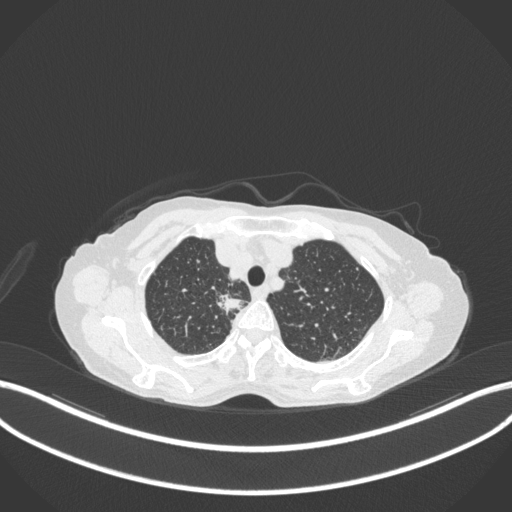
Chest CT, one axial slice. Position 309 of 363 along the scan axis. Reconstruction kernel B31f. 120 kVp. Lung window (W 1500 / L -600 HU). 1 mm slice thickness. 512 × 512 image matrix. Female patient, age 75 years. Case-level facts recorded for this patient, not image findings: clinical TNM (as recorded): T1c N1 M1.
Outlined on this slice (rectangle marked by the reading radiologist):
- lung tumour (recorded histology: adenocarcinoma): bounding box (x1, y1, x2, y2) in pixels: (215, 289, 249, 314)